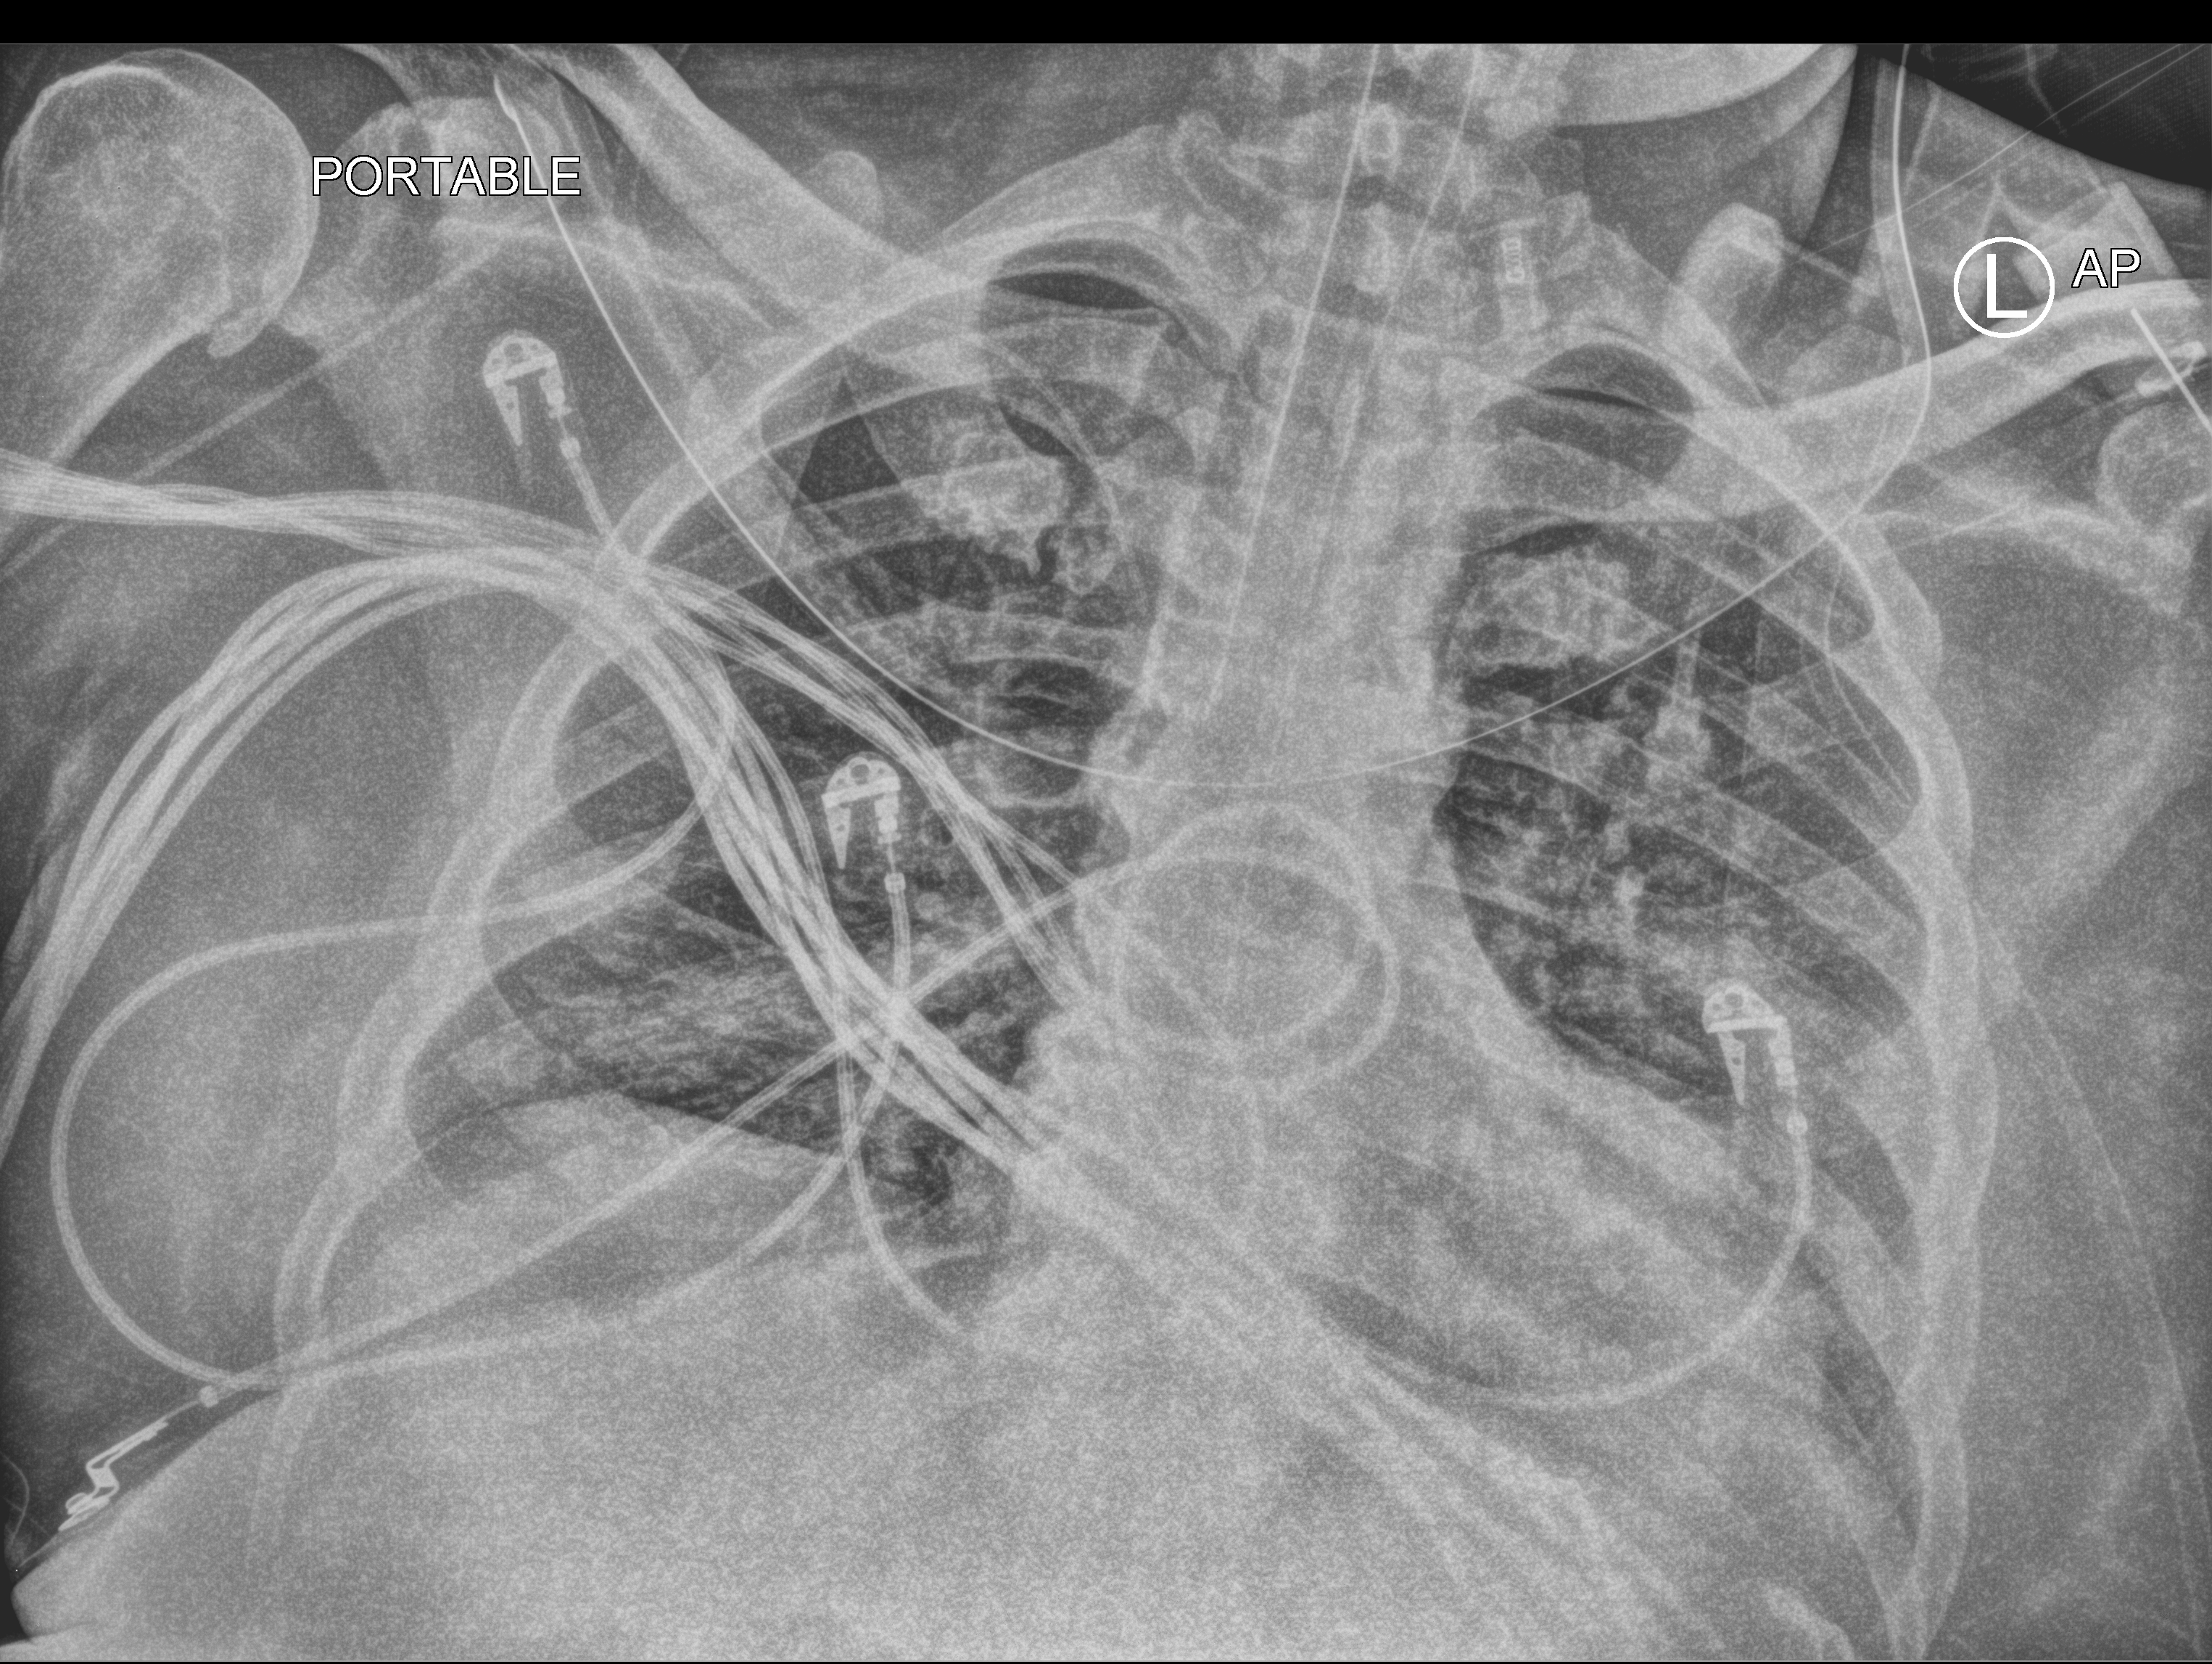
Bedside chest radiograph (computed radiography); anteroposterior (AP) projection. Male patient hospitalised with COVID-19, age 18–59 years.
Hospital-stay facts (about this admission, not read from this image; timing relative to this image not recorded): diabetes (admission record): no; mechanically ventilated during this hospital stay: yes.